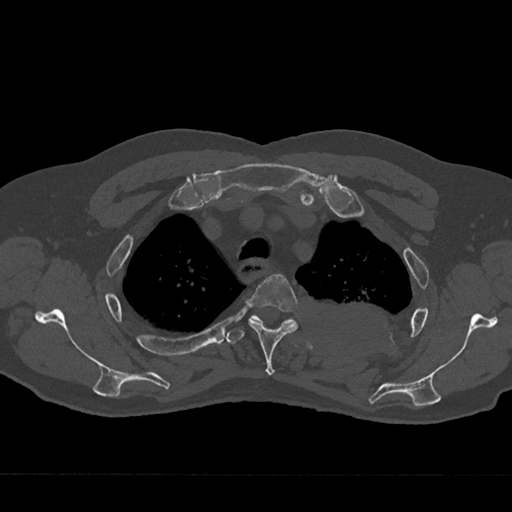
CT including the spine, one axial slice; position 556 of 797 along the scan axis; reconstruction kernel Br40s/3; 120 kVp; bone window (W 1800 / L 400 HU); 0.5 mm slice thickness; 512 × 512 image matrix. Patient: male, 75 years. From the clinical record (not read from this slice): primary cancer: renal; vertebrae with lytic lesions (as recorded): T4.
Outlined on this slice (semi-automatically segmented with operator editing):
- T3 vertebra: bounding box [x1, y1, x2, y2] px = [248, 274, 298, 376]
- T4 vertebra: [226, 314, 296, 344]